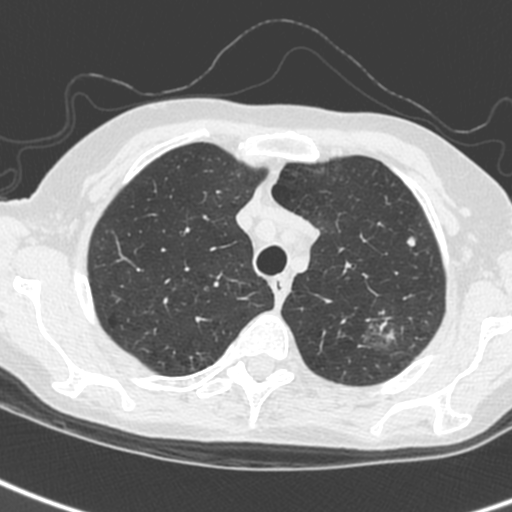
Low-dose screening chest CT, one axial slice. Slice 207 of 242 in the series (ordered by position). Lung window (W 1500 / L -600 HU). 1.3 mm slice thickness. 512 × 512 image matrix, field of view 284 × 284 mm.
Structures marked on this image (expert manual segmentation):
- lesion 2 (tumor, upper lobe of left lung): box from (x=407, y=237) to (x=415, y=247) px